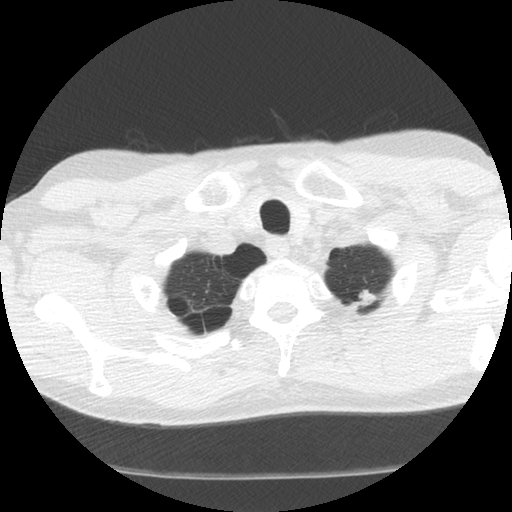
Chest CT (low-dose screening protocol), one axial image, baseline screening round, lung window (W 1500 / L -600 HU), 512 × 512 image matrix. Male participant, aged 63 years at enrolment. Former smoker at enrolment.
Lesion marked by an expert reader, bounding box [x1, y1, x2, y2] px = [342, 280, 387, 321]. The screening reader recorded 4 non-calcified nodules or masses ≥4 mm on this exam; which of them this box marks is not recorded. Official screen result: positive, change unspecified: nodule(s) >= 4 mm or enlarging nodule(s), mass(es), or other non-specific abnormalities suspicious for lung cancer. Lung cancer was diagnosed 629 days after this screen (after the second annual screen): adenocarcinoma, NOS, left upper lobe, moderately differentiated (G2), stage IB (AJCC 6th edition), 14 mm at pathology.